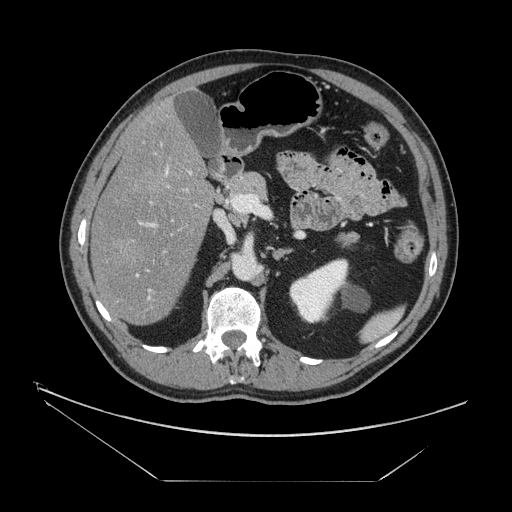
Contrast-enhanced abdominal CT, one axial slice. Position 78 of 161 along the scan axis. Reconstruction kernel STANDARD. Intravenous contrast given. Soft-tissue window (W 400 / L 40 HU). 512 × 512 image matrix, field of view 440 × 440 mm. Male patient, age 65 years. From the clinical record (not read from this slice): diagnosis: colorectal cancer liver metastases, imaged before liver resection; multiple liver metastases: yes; largest metastasis: 4.2 cm.
Structures marked on this image (expert manual segmentation):
- hepatic veins: bounding box [x1, y1, x2, y2] px = [132, 165, 181, 300]
- liver: [91, 102, 213, 325]
- planned liver remnant (the part of the liver to remain after resection): [113, 106, 203, 324]
- portal vein (with intrahepatic branches): [111, 171, 203, 316]